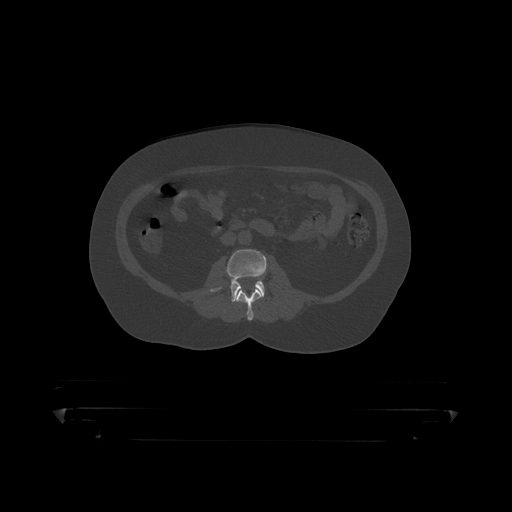
CT including the spine, one axial slice. 120 kVp. Bone window (W 1800 / L 400 HU). 1.25 mm slice thickness. 512 × 512 image matrix, field of view 650 × 650 mm. Patient: male, 60 years. From the clinical record (not read from this slice): primary cancer: prostate.
Structures marked on this image (semi-automatically segmented with operator editing):
- L2 vertebra: bounding box [x1, y1, x2, y2] px = [236, 288, 263, 319]
- L3 vertebra: [211, 249, 267, 302]